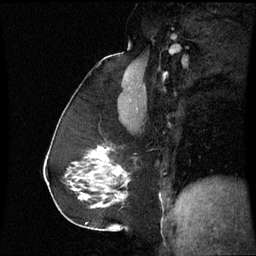
Breast MRI (dynamic contrast-enhanced), one sagittal slice; position 36 of 60 along the scan axis; dynamic contrast-enhanced series, image 2 of 3 at this slice position (ordered by acquisition); 1.5 T; TE 4.2 ms, TR 8.9 ms; 2.4 mm slice thickness; 256 × 256 image matrix. Female patient, age 59 years. From the clinical record (not read from this slice): setting: breast cancer imaged before/during neoadjuvant chemotherapy; receptor status: triple-negative.
Outlined on this slice (semi-automatically segmented with operator editing):
- analysis volume of interest (the breast-tissue region the enhancement analysis was run in; not a lesion): bounding box [x1, y1, x2, y2] px = [88, 146, 131, 197]
- tumour enhancement mask (voxels above the 70 % enhancement threshold inside the analysis volume of interest): [106, 164, 121, 173]